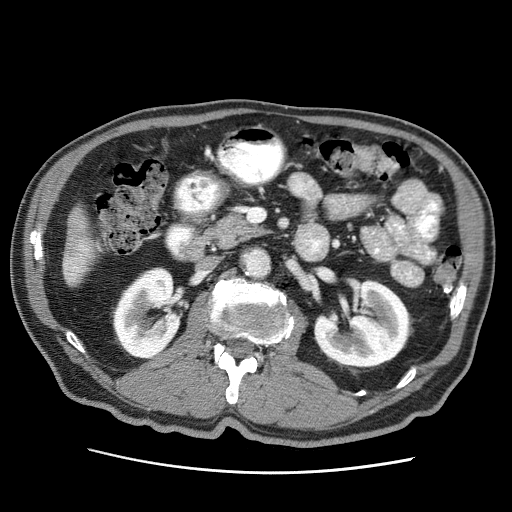
Contrast-enhanced abdominal CT (liver protocol), one axial slice. Position 7 of 75 along the scan axis. Soft-tissue window (W 400 / L 40 HU). 2.5 mm slice thickness. 512 × 512 image matrix, field of view 360 × 360 mm. Case-level facts recorded for this patient, not image findings: diagnosis: hepatocellular carcinoma (patient treated with transarterial chemoembolisation; whether this scan precedes or follows treatment is not stated here); TNM stage (as recorded): Stage-IIIA; Child-Pugh class: A; tumour differentiation: well differentiated; tumour nodularity: multinodular.
Outlined on this slice (semi-automatically segmented with operator editing):
- liver parenchyma outside the tumour (the mass and vessels are separate outlines, so this box may not span the whole liver): bounding box [x1, y1, x2, y2] px = [62, 212, 92, 284]
- liver vessels: [69, 244, 83, 276]